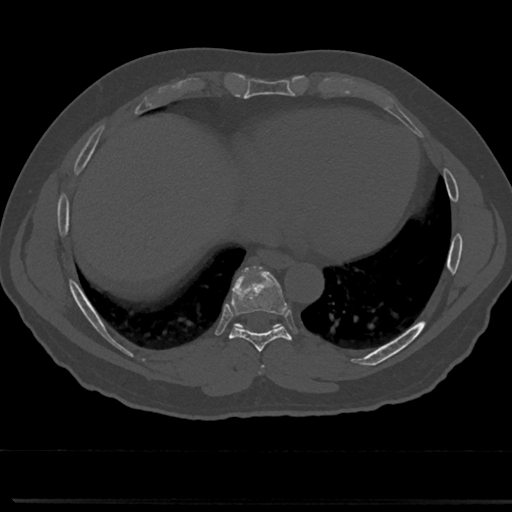
CT including the spine, one axial slice. Position 345 of 817 along the scan axis. 120 kVp. Bone window (W 1800 / L 400 HU). 0.5 mm slice thickness. 512 × 512 image matrix, field of view 355 × 355 mm. Male patient, age 61 years. From the clinical record (not read from this slice): primary cancer: prostate.
Structures marked on this image (semi-automatic segmentation, software-assisted and operator-edited):
- T7 vertebra: bounding box [x1, y1, x2, y2] px = [255, 341, 269, 376]
- T8 vertebra: [216, 271, 304, 353]